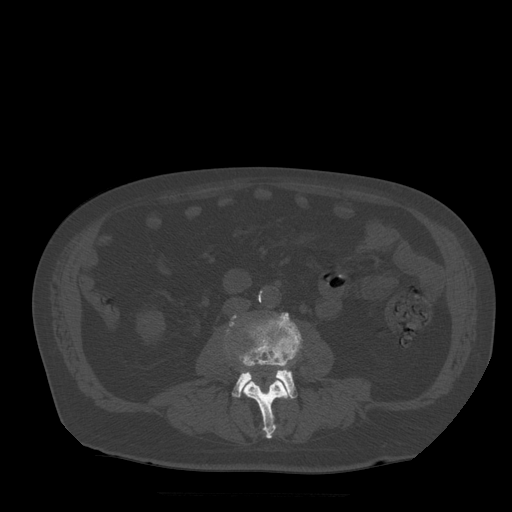
CT including the spine, one axial slice; slice 129 of 522 in the series (ordered by position); bone window (W 1800 / L 400 HU); 512 × 512 image matrix, field of view 420 × 420 mm. Patient age 72 years. Case-level facts recorded for this patient, not image findings: primary cancer: prostate.
Structures marked on this image (semi-automatic segmentation, software-assisted and operator-edited):
- L3 vertebra: bounding box [x1, y1, x2, y2] px = [241, 362, 292, 439]
- L4 vertebra: [230, 313, 302, 399]